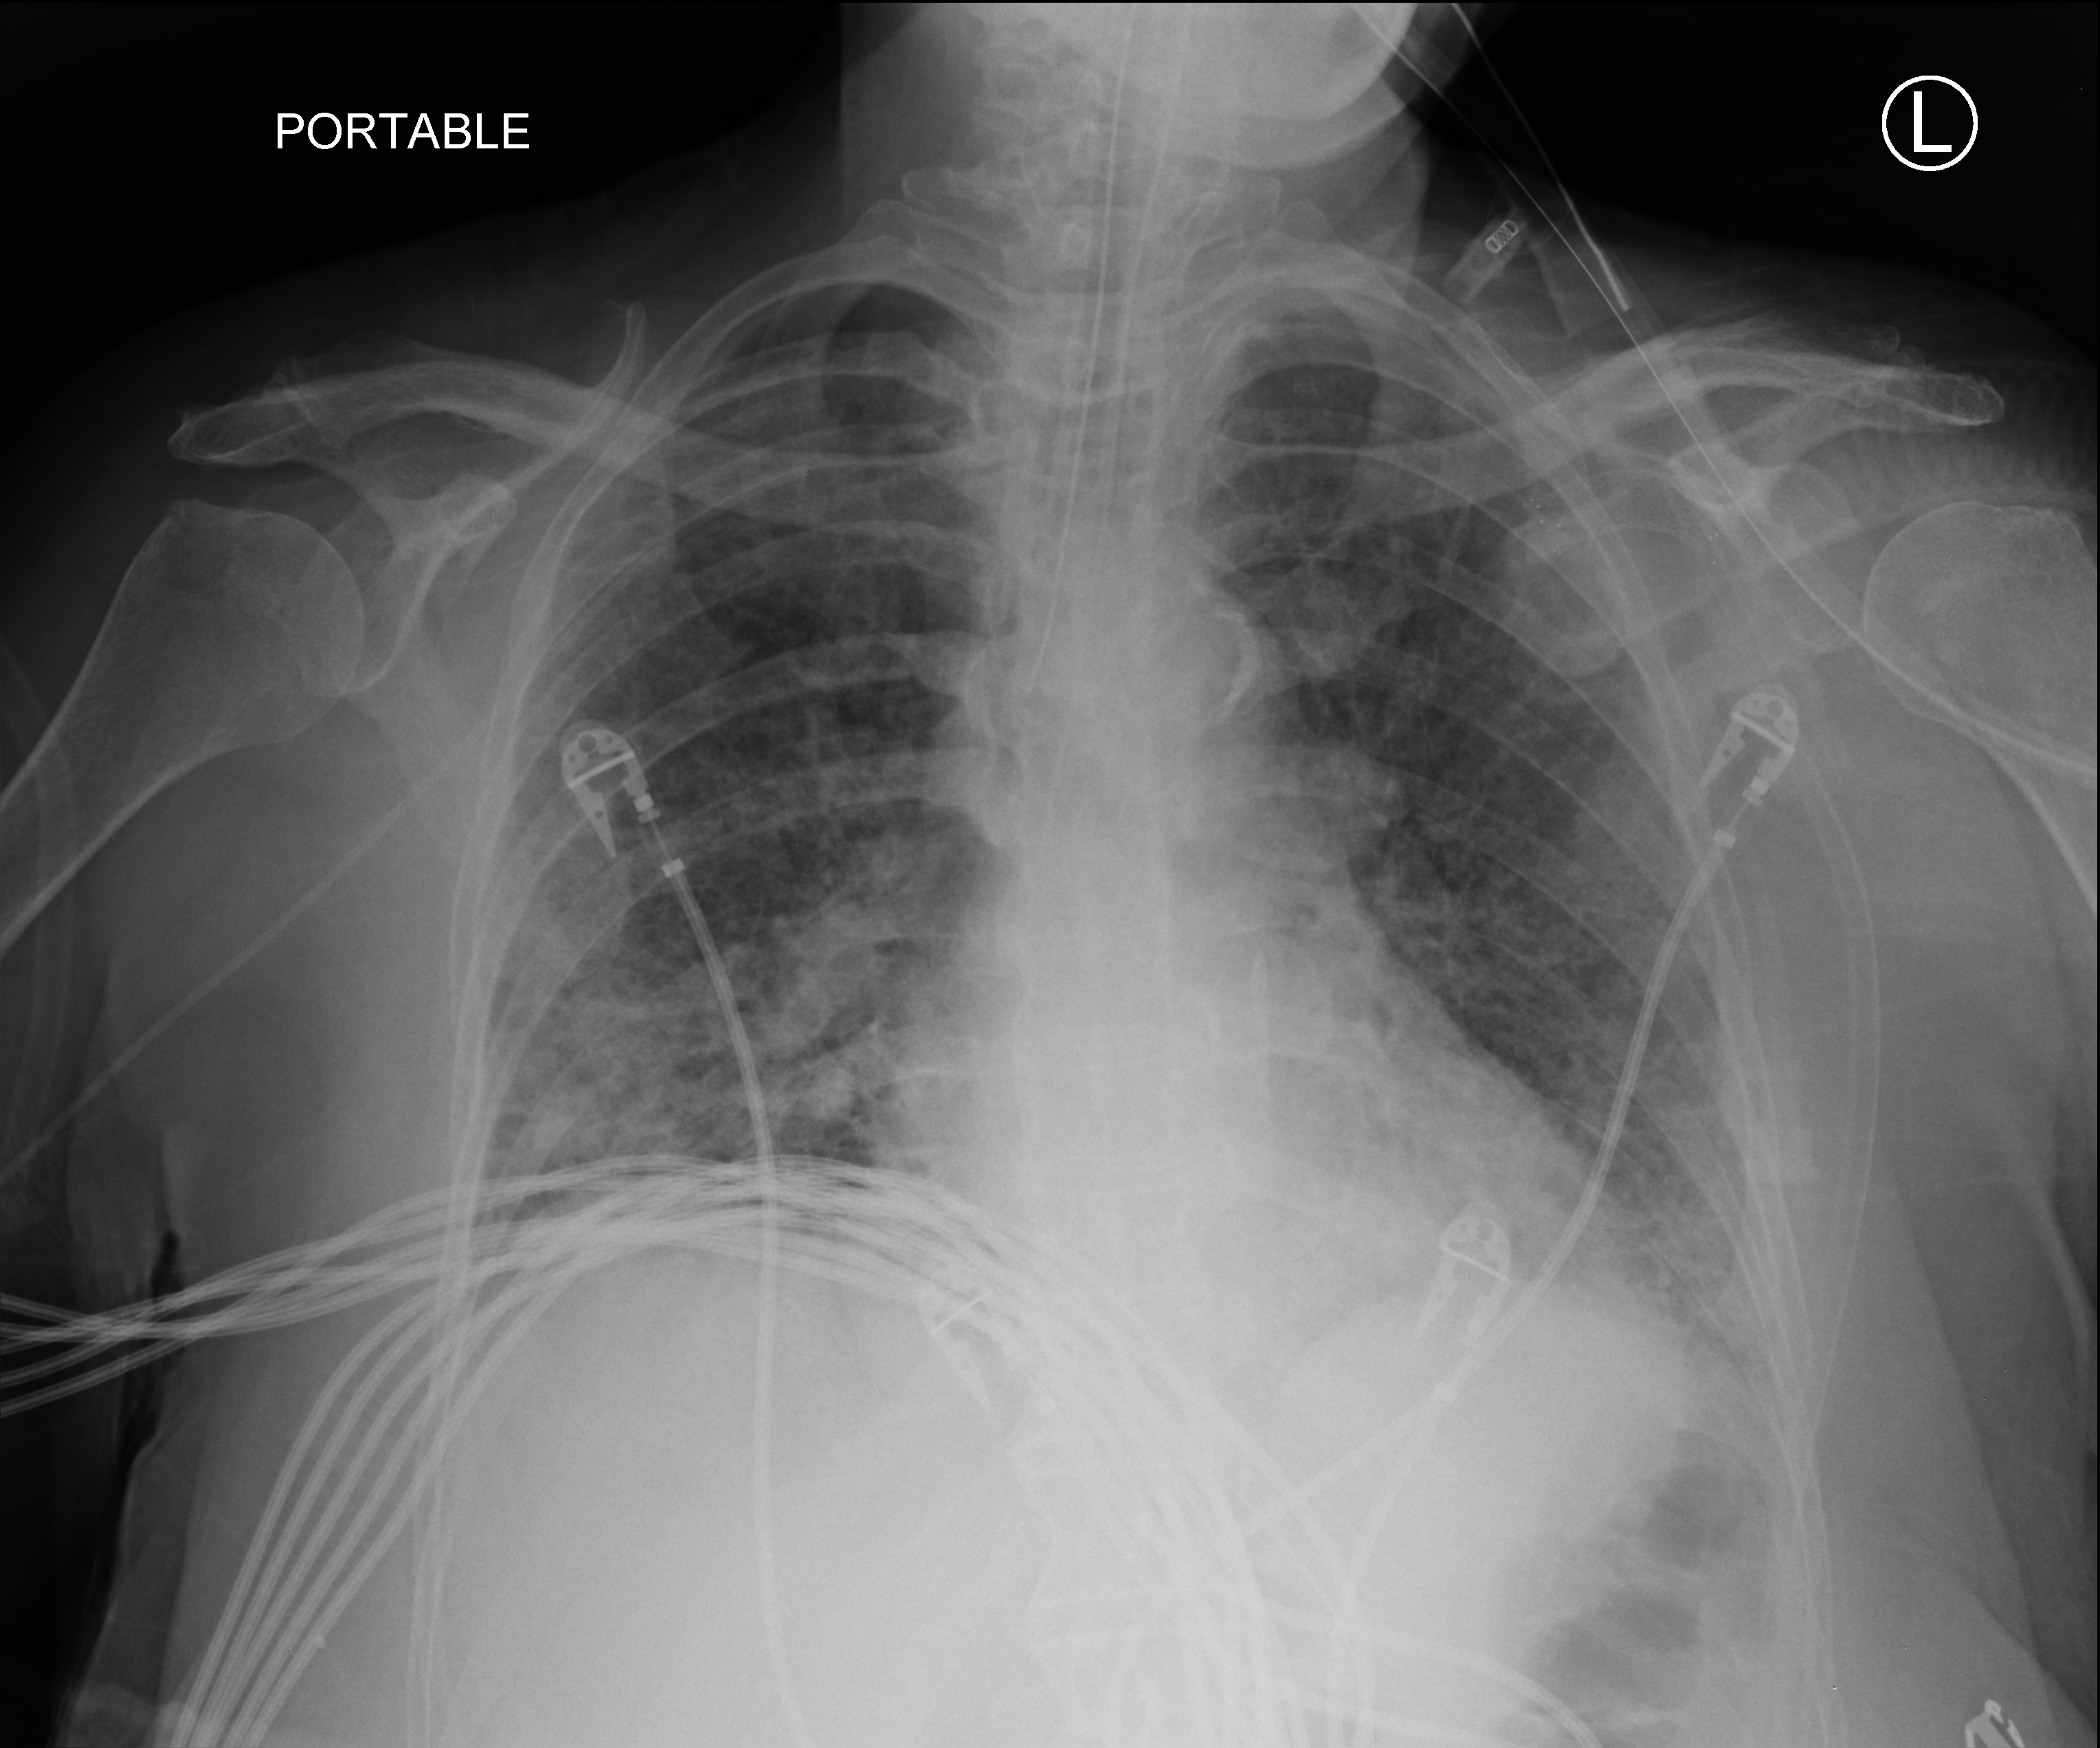
Portable chest radiograph; anteroposterior (AP) projection. Patient hospitalised with COVID-19; female, aged 60–74 years.
From the hospital-stay record, not from the radiograph (when in the stay this image was taken is not recorded): other chronic lung disease (admission record): no.